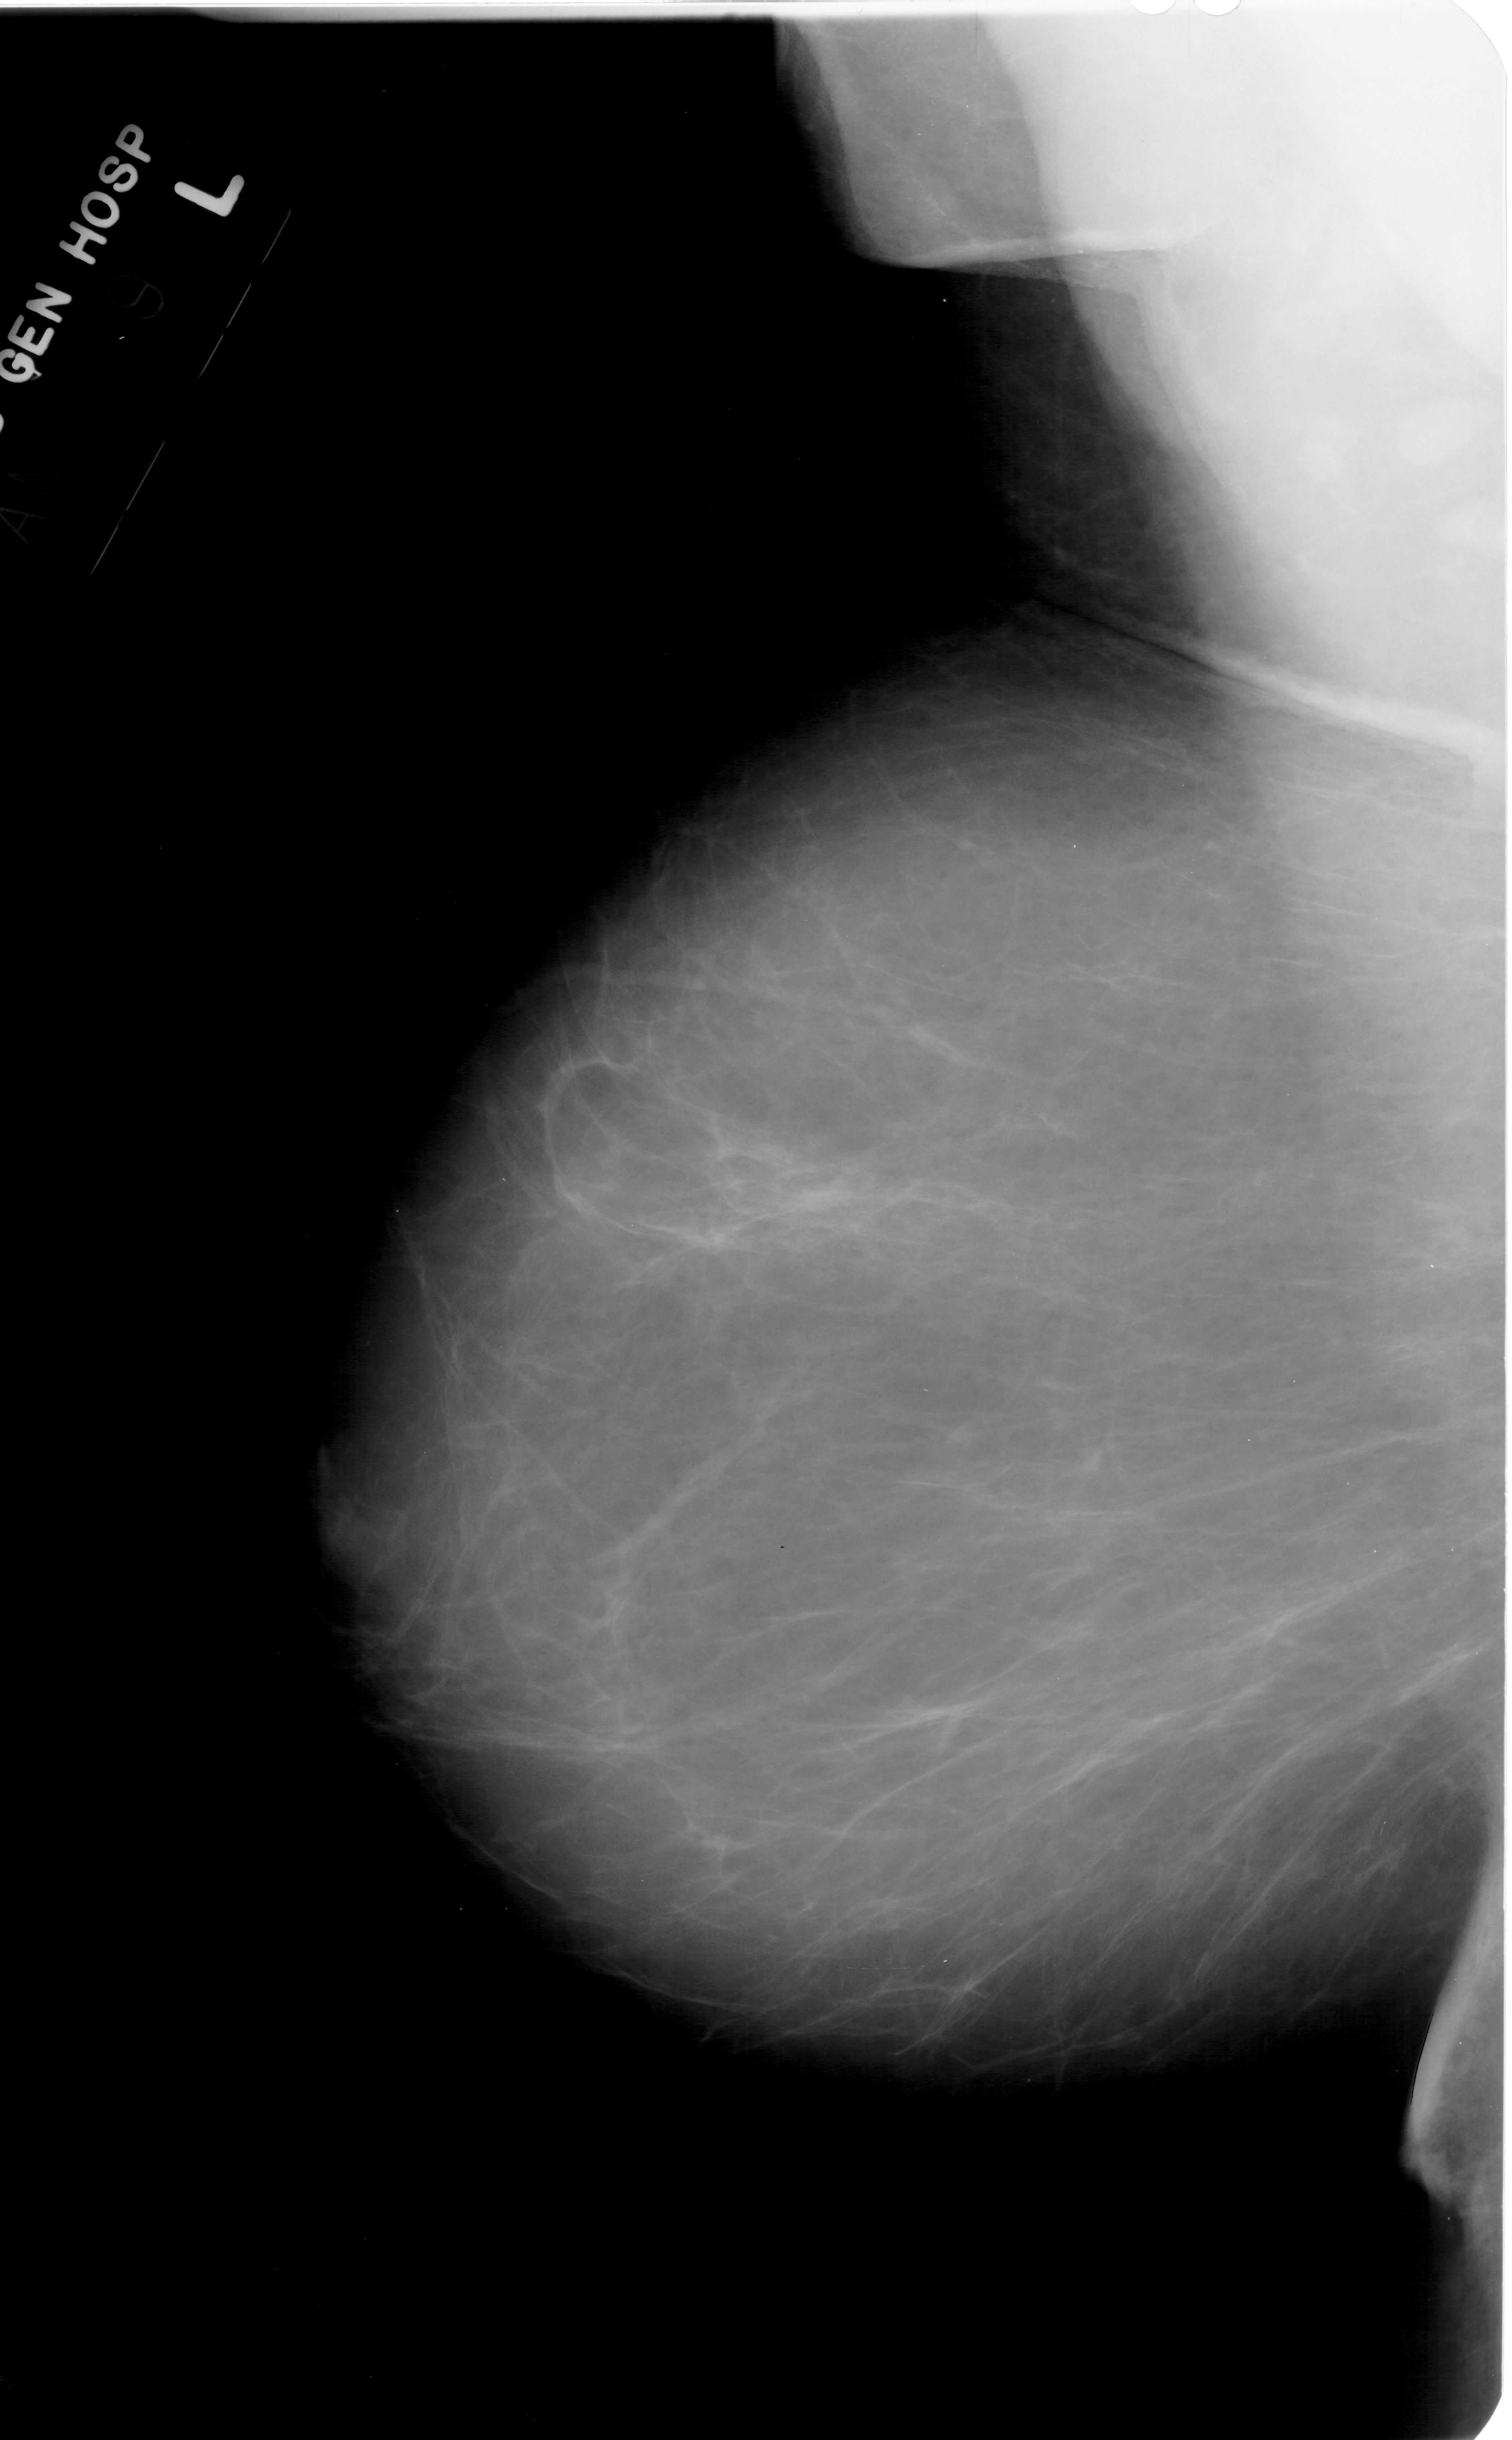
Scanned film-screen mammogram, left breast, mediolateral oblique (MLO) view, breast composition: almost entirely fatty (BI-RADS density category 1 of 4).
Mass, shape irregular, margins ill defined; BI-RADS assessment category 2; subtlety rating 2 on a 1 (subtle) to 5 (obvious) scale; pathology result (as recorded, not read from the image): benign.